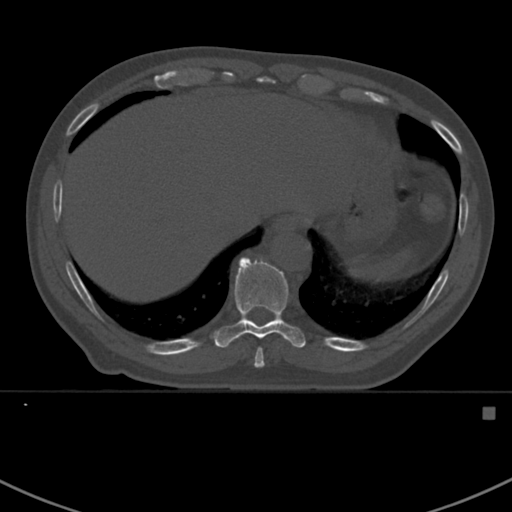
CT including the spine, one axial slice. 120 kVp. Bone window (W 1800 / L 400 HU). 1.5 mm slice thickness. 512 × 512 image matrix, field of view 358 × 358 mm. Patient: male, 59 years. Case-level facts recorded for this patient, not image findings: primary cancer: prostate.
Outlined on this slice (semi-automatic segmentation, software-assisted and operator-edited):
- T10 vertebra: bounding box <212,256,305,368> (left, top, right, bottom; pixels)
- T9 vertebra: <255,348,263,365>